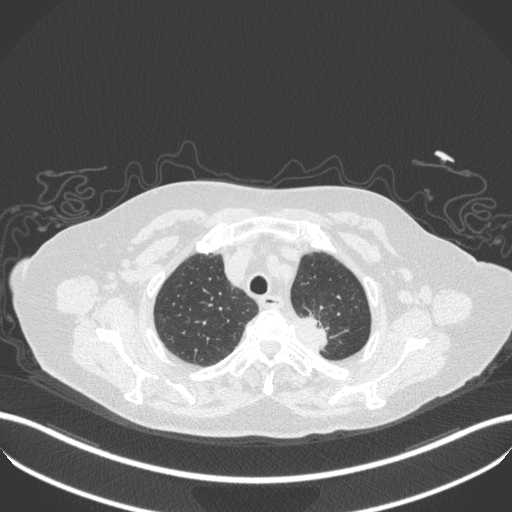
Chest CT, one axial slice. Position 286 of 353 along the scan axis. Reconstruction kernel B31f. 100 kVp. Lung window (W 1500 / L -600 HU). 512 × 512 image matrix, field of view 400 × 400 mm. Female patient, age 81 years. Case-level facts recorded for this patient, not image findings: clinical TNM (as recorded): T2a N0 M0.
Outlined on this slice (bounding box drawn by a radiologist):
- lung tumour (recorded histology: adenocarcinoma): bounding box [x1, y1, x2, y2] px = [281, 309, 338, 353]